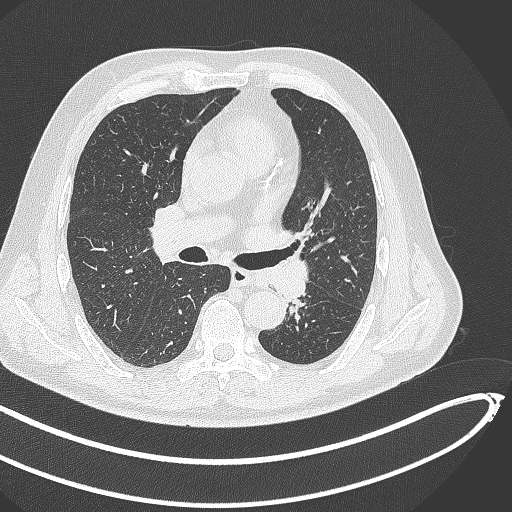
Chest CT, one axial slice. Position 267 of 468 along the scan axis. Lung window (W 1500 / L -600 HU). 1 mm slice thickness. 512 × 512 image matrix, field of view 400 × 400 mm. Male patient, age 64 years. Case-level facts recorded for this patient, not image findings: clinical TNM (as recorded): T1c N0 M0.
Outlined on this slice (bounding box drawn by a radiologist):
- lung tumour (recorded histology: squamous cell carcinoma): bounding box <265,251,309,303> (left, top, right, bottom; pixels)